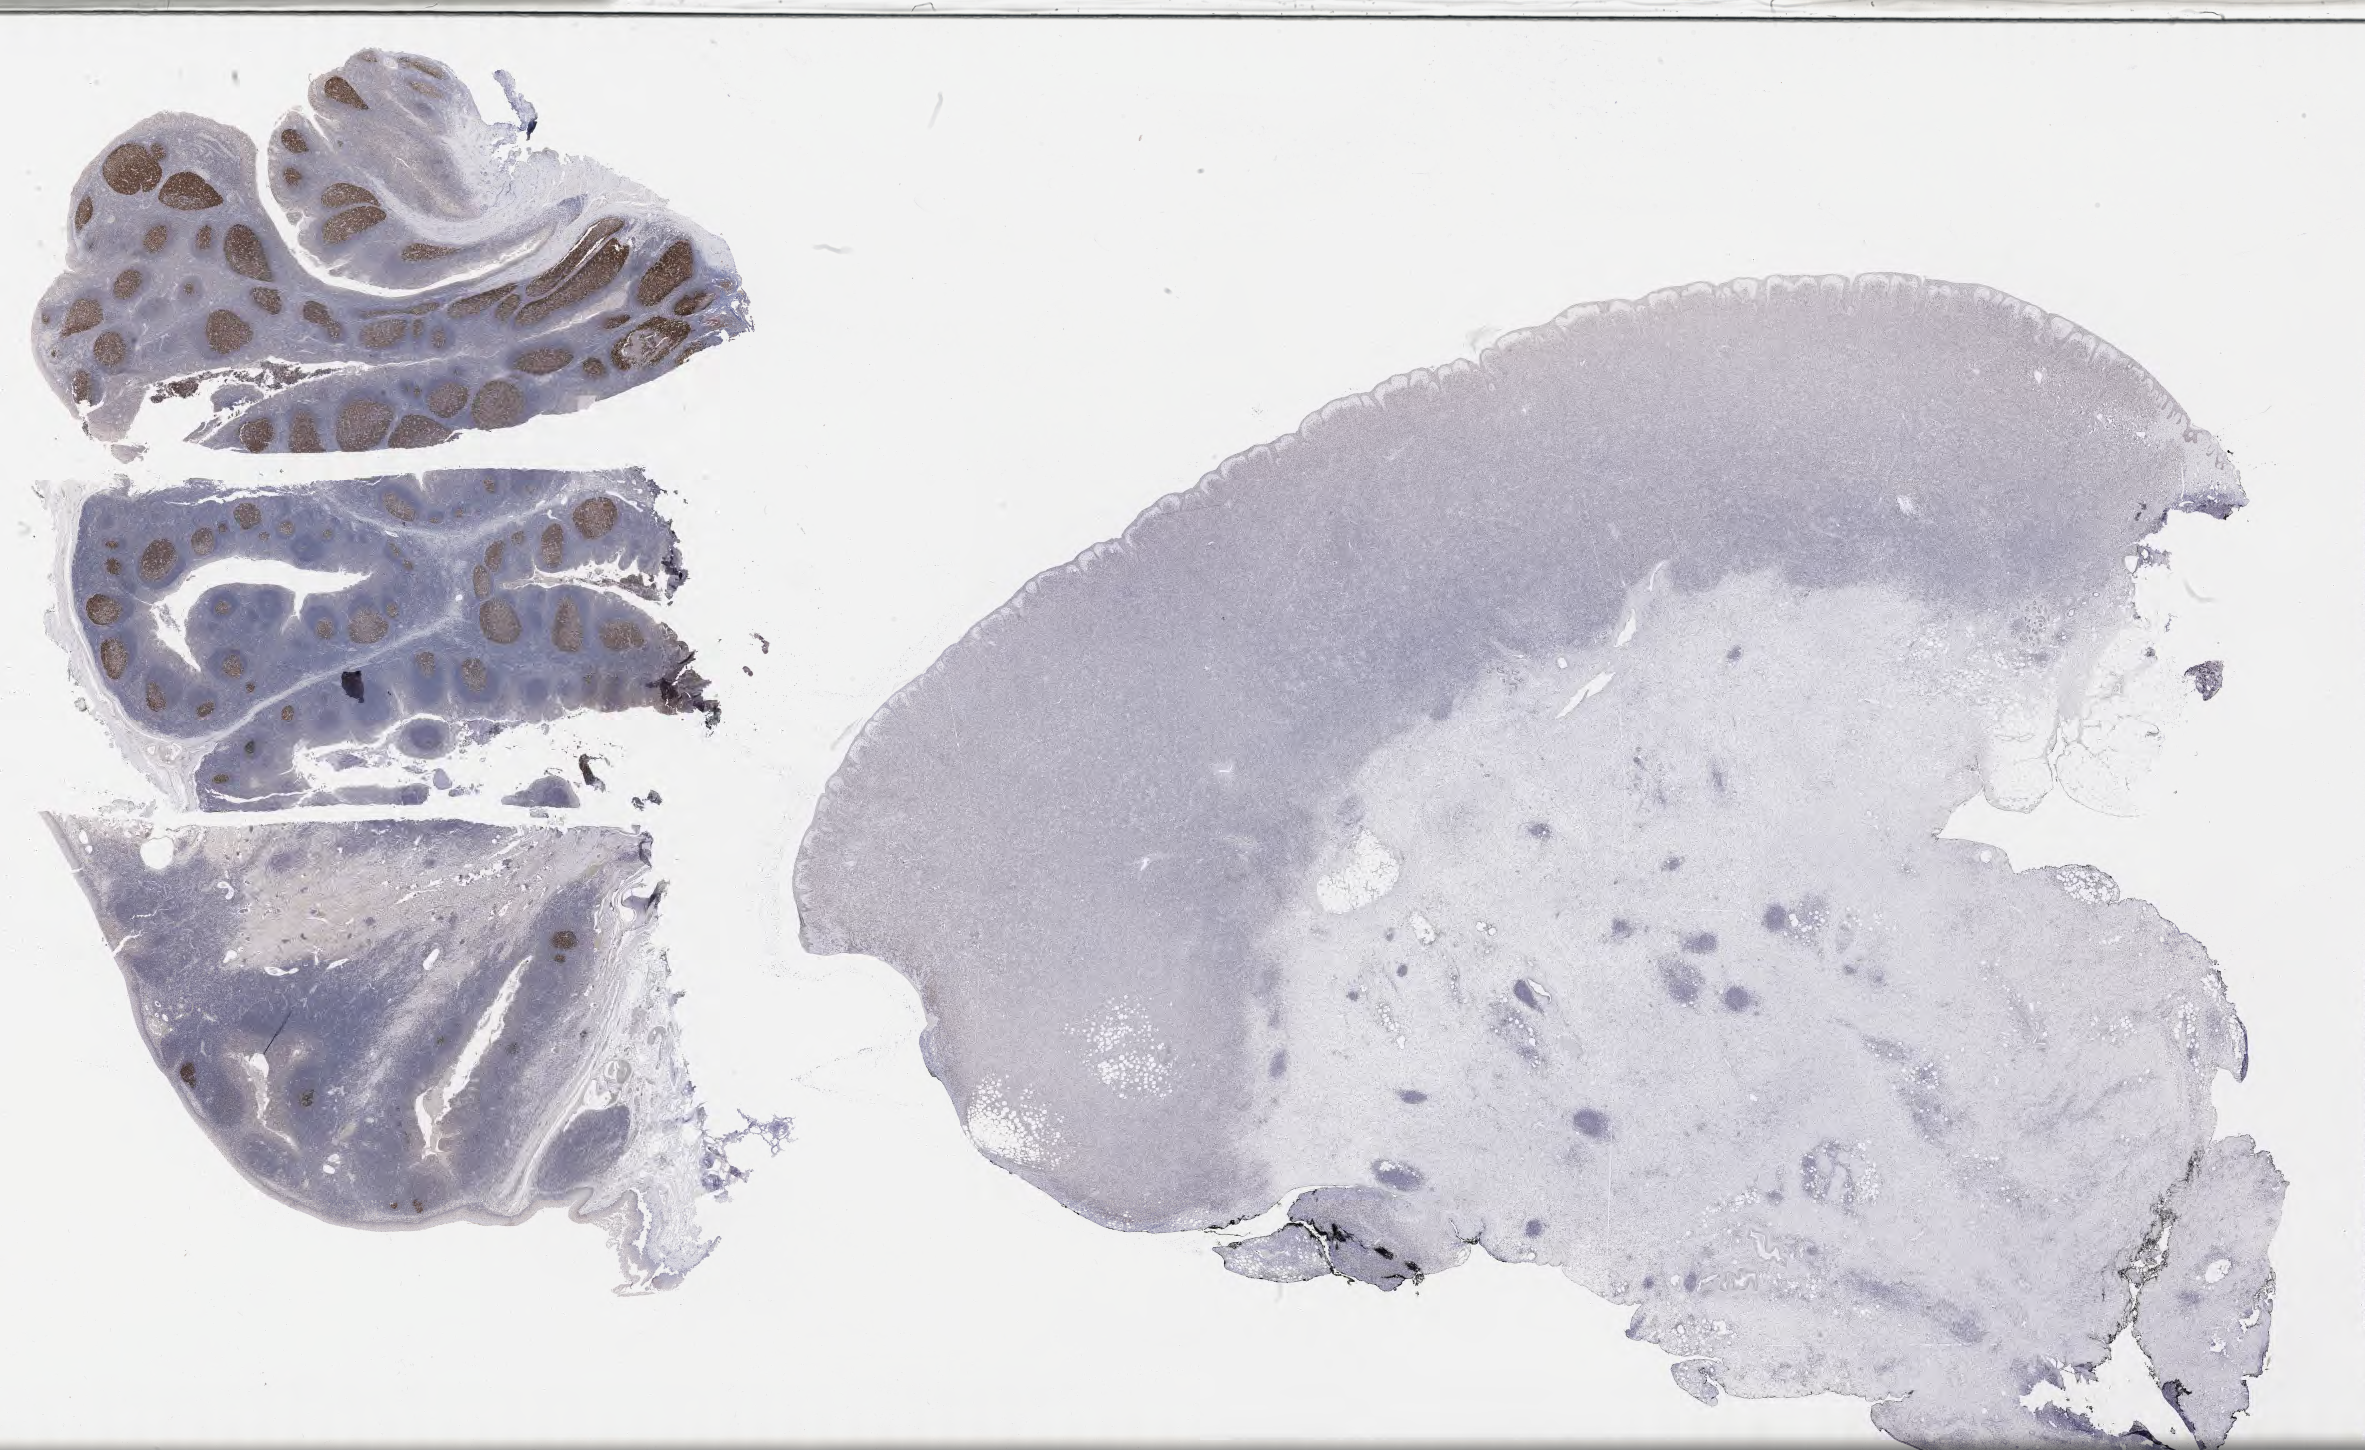
Whole-slide image, immunohistochemical stain for BCL6 — low-resolution overview of the scanned area, about 38.2 x 23.4 mm; tumor tissue; site: lymph node. Patient male; aged 52.
Diagnosis: Diffuse large B-cell lymphoma, NOS.